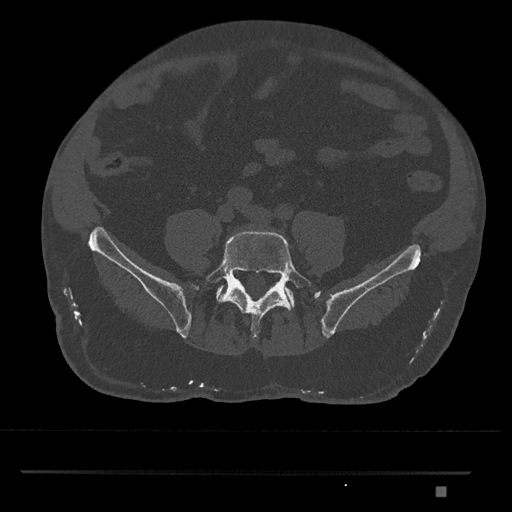
CT including the spine, one axial slice. Slice 554 of 1134 in the series (ordered by position). Bone window (W 1800 / L 400 HU). 0.5 mm slice thickness. 512 × 512 image matrix, field of view 429 × 429 mm. Male patient, age 65 years. From the clinical record (not read from this slice): primary cancer: prostate.
Structures marked on this image (semi-automatically segmented with operator editing):
- L5 vertebra: box from (x=206, y=230) to (x=314, y=339) px